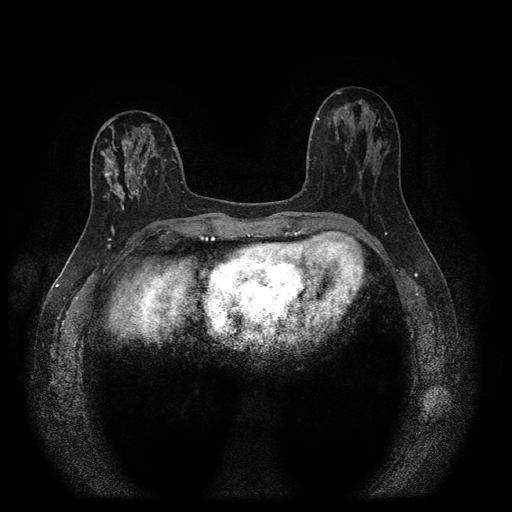
Breast MRI (dynamic contrast-enhanced, multi-phase), one axial slice; slice 41 of 116 in the series (ordered by position); dynamic contrast-enhanced series, time point 2 of 5 at this slice position (early post-contrast); 1.5 T; TE 2.7 ms, TR 5.4 ms; 2 mm slice thickness; 512 × 512 image matrix. Patient: female, 47 years.
Structures marked on this image (semi-automatic segmentation, software-assisted and operator-edited):
- breast lesion (labelled 'tumour' in the annotation; benign lesions carry a separate 'benign' label): bounding box (x1, y1, x2, y2) in pixels: (100, 125, 159, 207)